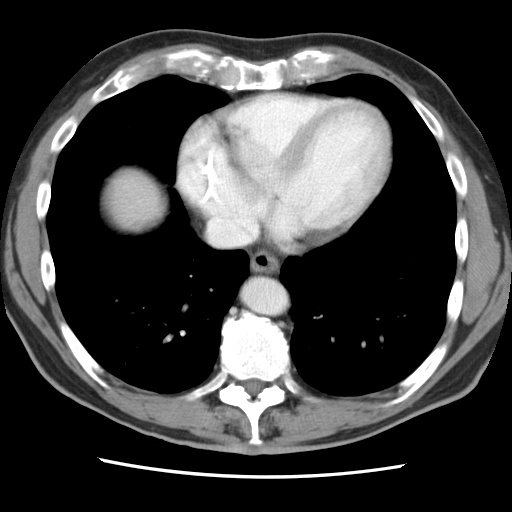
Contrast-enhanced abdominal CT, one axial slice. Slice 83 of 83 in the series (ordered by position). Intravenous contrast given. Soft-tissue window (W 400 / L 40 HU). 5 mm slice thickness. 512 × 512 image matrix, field of view 321 × 321 mm. Male patient, age 69 years. From the clinical record (not read from this slice): diagnosis: colorectal cancer liver metastases, imaged before liver resection.
Structures marked on this image (outlined manually by an expert reader):
- liver: bounding box <103,168,161,230> (left, top, right, bottom; pixels)
- planned liver remnant (the part of the liver to remain after resection): <104,169,162,229>